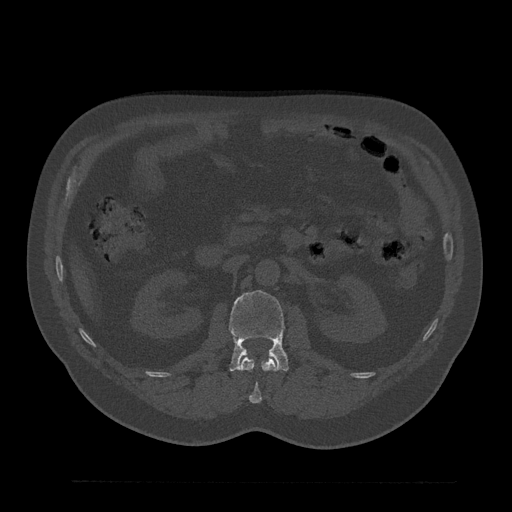
CT including the spine, one axial slice. Slice 124 of 797 in the series (ordered by position). Reconstruction kernel Br40s/3. 120 kVp. Bone window (W 1800 / L 400 HU). 0.5 mm slice thickness. 512 × 512 image matrix. Patient: male, 61 years. From the clinical record (not read from this slice): primary cancer: prostate.
Annotated regions visible in this slice (semi-automatic segmentation, software-assisted and operator-edited):
- L1 vertebra: bounding box <240,357,278,403> (left, top, right, bottom; pixels)
- L2 vertebra: <229,290,289,371>